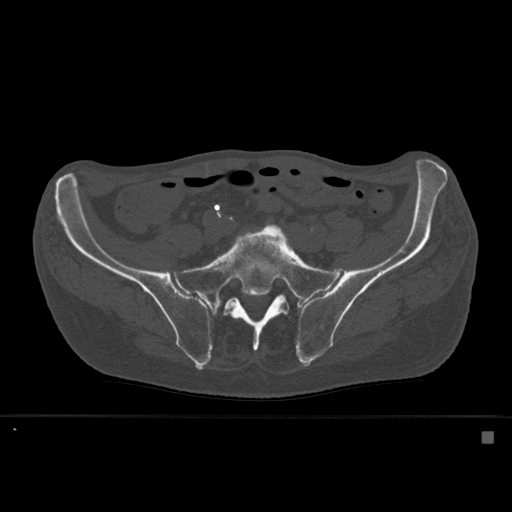
CT including the spine, one axial slice; position 157 of 527 along the scan axis; bone window (W 1800 / L 400 HU); 1.5 mm slice thickness; 512 × 512 image matrix, field of view 373 × 373 mm. Patient: male, 78 years. Case-level facts recorded for this patient, not image findings: primary cancer: prostate.
Outlined on this slice (semi-automatically segmented with operator editing):
- L5 vertebra: bounding box (x1, y1, x2, y2) in pixels: (281, 303, 289, 314)